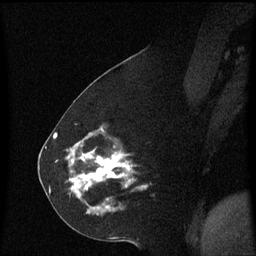
Breast MRI (dynamic contrast-enhanced), one sagittal slice. Position 27 of 60 along the scan axis. Dynamic contrast-enhanced series, image 2 of 3 at this slice position (ordered by acquisition). 1.5 T. TE 4.2 ms, TR 8.4 ms. 2.2 mm slice thickness. 256 × 256 image matrix. Patient: female, 60 years. Case-level facts recorded for this patient, not image findings: setting: breast cancer imaged before/during neoadjuvant chemotherapy; receptor status: triple-negative.
Outlined on this slice (semi-automatically segmented with operator editing):
- analysis volume of interest (the breast-tissue region the enhancement analysis was run in; not a lesion): bounding box <68,142,140,215> (left, top, right, bottom; pixels)
- tumour enhancement mask (voxels above the 70 % enhancement threshold inside the analysis volume of interest): <72,150,132,193>